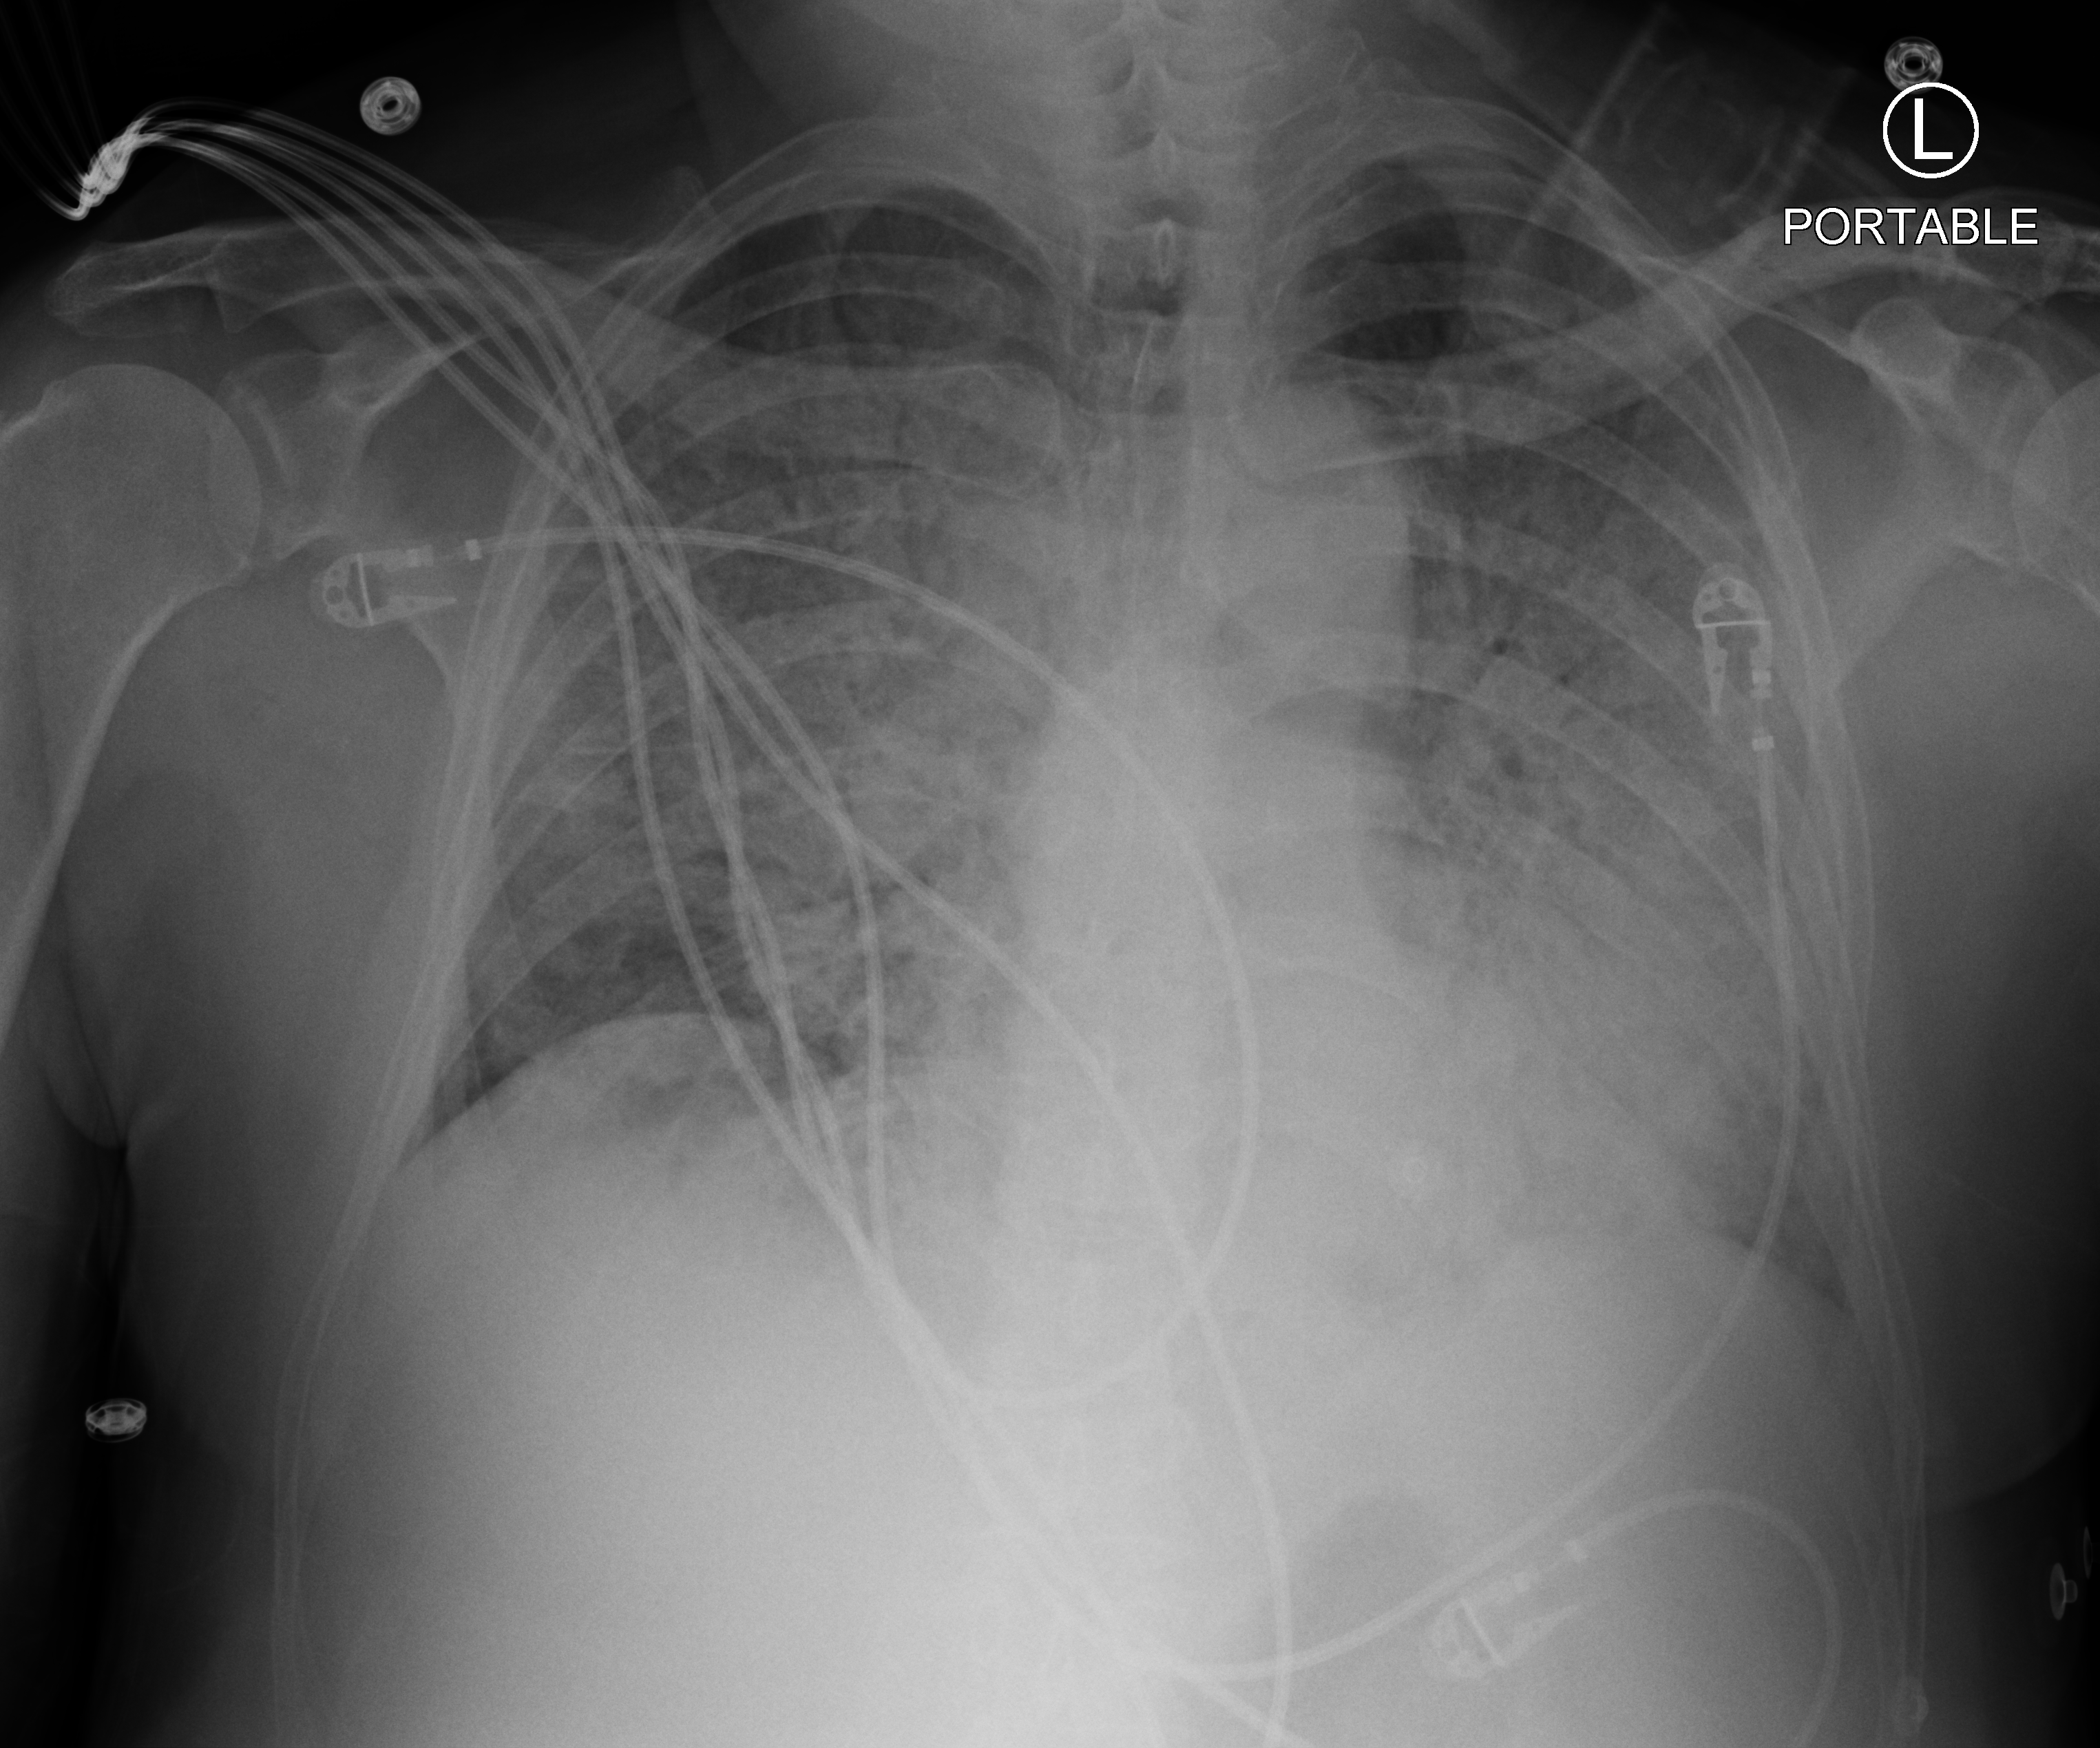
Chest X-ray (portable). Patient hospitalised with COVID-19; male, aged 60–74 years.
Admission-level facts for this patient (not findings on this image; timing relative to this image not recorded):
- other chronic lung disease (admission record): no
- admitted to intensive care during this hospital stay: yes
- mechanically ventilated during this hospital stay: yes